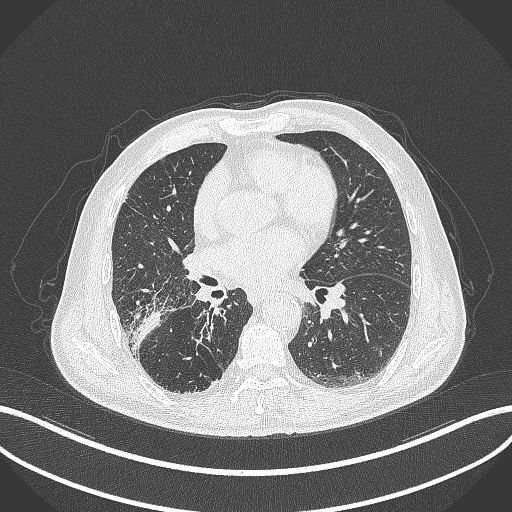
Chest CT, one axial slice; slice 201 of 429 in the series (ordered by position); 120 kVp; lung window (W 1500 / L -600 HU); 1 mm slice thickness; 512 × 512 image matrix, field of view 400 × 400 mm. Male patient, age 72 years. Case-level facts recorded for this patient, not image findings: clinical TNM (as recorded): T3 N2 M0.
Outlined on this slice (rectangle marked by the reading radiologist):
- lung tumour (recorded histology: adenocarcinoma): bounding box (x1, y1, x2, y2) in pixels: (129, 308, 162, 351)